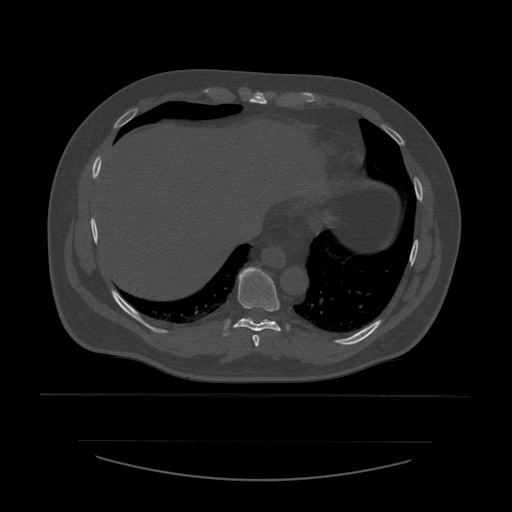
CT including the spine, one axial slice; reconstruction kernel STANDARD; bone window (W 1800 / L 400 HU); 512 × 512 image matrix, field of view 441 × 441 mm. Patient age 44 years. Case-level facts recorded for this patient, not image findings: primary cancer: soft tissue sarcoma.
Structures marked on this image (semi-automatic segmentation, software-assisted and operator-edited):
- T8 vertebra: bounding box (x1, y1, x2, y2) in pixels: (252, 335, 260, 347)
- T9 vertebra: (224, 267, 290, 337)